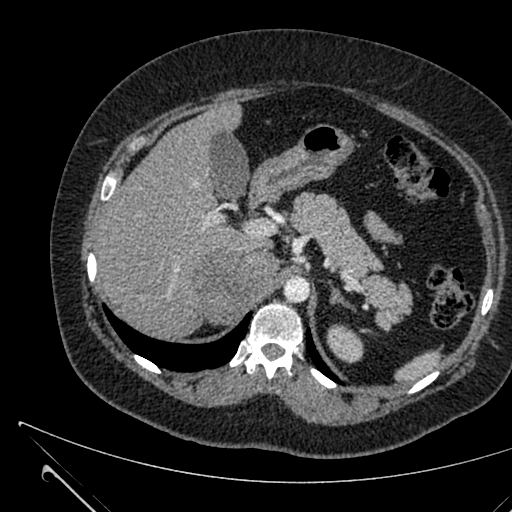
Contrast-enhanced abdominal CT, one axial slice; 120 kVp; intravenous contrast given; soft-tissue window (W 400 / L 40 HU); 1 mm slice thickness; 512 × 512 image matrix, field of view 376 × 376 mm. Female patient, age 36 years. Case-level facts recorded for this patient, not image findings: diagnosis: adrenocortical carcinoma; tumour side: right adrenal; tumour size at pathology: 10 cm; Ki-67 index: 20 %; stage (as recorded): 4.
Structures marked on this image (semi-automatically segmented with operator editing):
- mass: bounding box (x1, y1, x2, y2) in pixels: (197, 250, 280, 323)